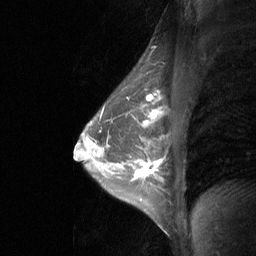
Breast MRI (dynamic contrast-enhanced), one sagittal slice; dynamic contrast-enhanced study with each time point stored as its own series, time point 2 of 3 at this slice position (early post-contrast, ordered by acquisition time); 1.5 T; TE 4.8 ms, TR 27 ms; 256 × 256 image matrix, field of view 200 × 200 mm. Female patient, age 47 years. Case-level facts recorded for this patient, not image findings: setting: breast cancer imaged before/during neoadjuvant chemotherapy; receptor status: HR-positive, HER2-negative.
Annotated regions visible in this slice (semi-automatically segmented with operator editing):
- analysis volume of interest (the breast-tissue region the enhancement analysis was run in; not a lesion): bounding box [x1, y1, x2, y2] px = [120, 142, 160, 203]
- tumour enhancement mask (voxels above the 90 % enhancement threshold inside the analysis volume of interest): [135, 163, 153, 177]